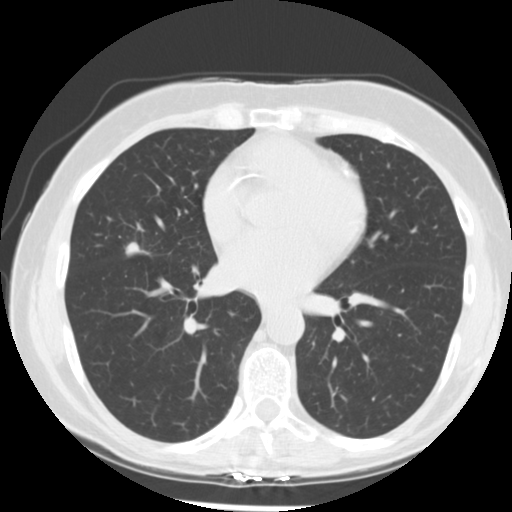
Chest CT (low-dose screening protocol), one axial image, baseline annual screen, lung window (W 1500 / L -600 HU), 2.5 mm slice thickness, standard (soft-tissue) reconstruction kernel (STANDARD), slice 128 of 255 in the series, 512 × 512 image matrix. Female, age 66 years at enrolment. Former smoker at enrolment.
Expert reader's lesion annotation, bounding box [x1, y1, x2, y2] px = [116, 229, 167, 267]. Reader record for this screening exam (exam-level; its link to the box is not recorded): non-calcified nodule or mass ≥4 mm, right middle lobe, 15 × 13 mm, poorly defined margins, soft tissue attenuation. Participant outcome: lung cancer diagnosed 27 days after this screen — adenocarcinoma, NOS, right middle lobe, undifferentiated (G4), stage IIIA (AJCC 6th edition), 18 mm at pathology.